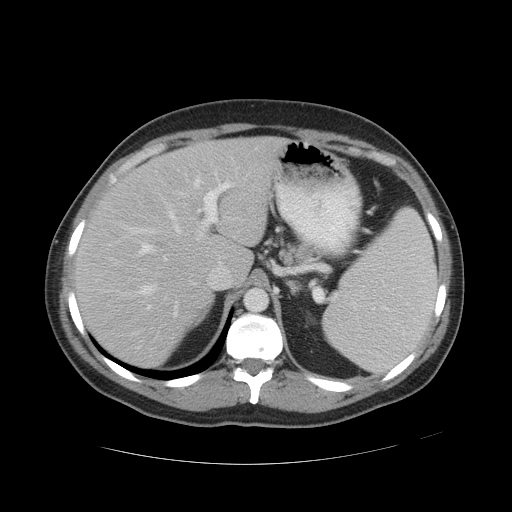
Contrast-enhanced abdominal CT, one axial slice. Position 35 of 49 along the scan axis. Reconstruction kernel STANDARD. Intravenous contrast given. Soft-tissue window (W 400 / L 40 HU). 5 mm slice thickness. 512 × 512 image matrix. Male patient, age 42 years. Case-level facts recorded for this patient, not image findings: diagnosis: colorectal cancer liver metastases, imaged before liver resection; multiple liver metastases: yes; largest metastasis: 2.8 cm; chemotherapy before resection: yes.
Annotated regions visible in this slice (expert manual segmentation):
- hepatic veins: box from (x=127, y=158) to (x=239, y=295) px
- liver: (x=77, y=138)–(x=276, y=367)
- planned liver remnant (the part of the liver to remain after resection): (x=77, y=138)–(x=276, y=367)
- portal vein (with intrahepatic branches): (x=128, y=173)–(x=234, y=309)